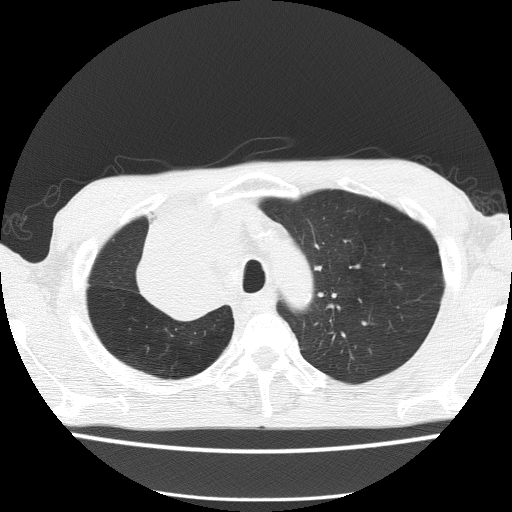
Low-dose screening chest CT, one axial slice. Slice 118 of 150 in the series (ordered by position). Reconstruction kernel FC51. 120 kVp. Lung window (W 1500 / L -600 HU). 512 × 512 image matrix.
Outlined on this slice (expert manual segmentation):
- lesion 1 (tumor, hilum of right lung): bounding box <137,203,221,320> (left, top, right, bottom; pixels)